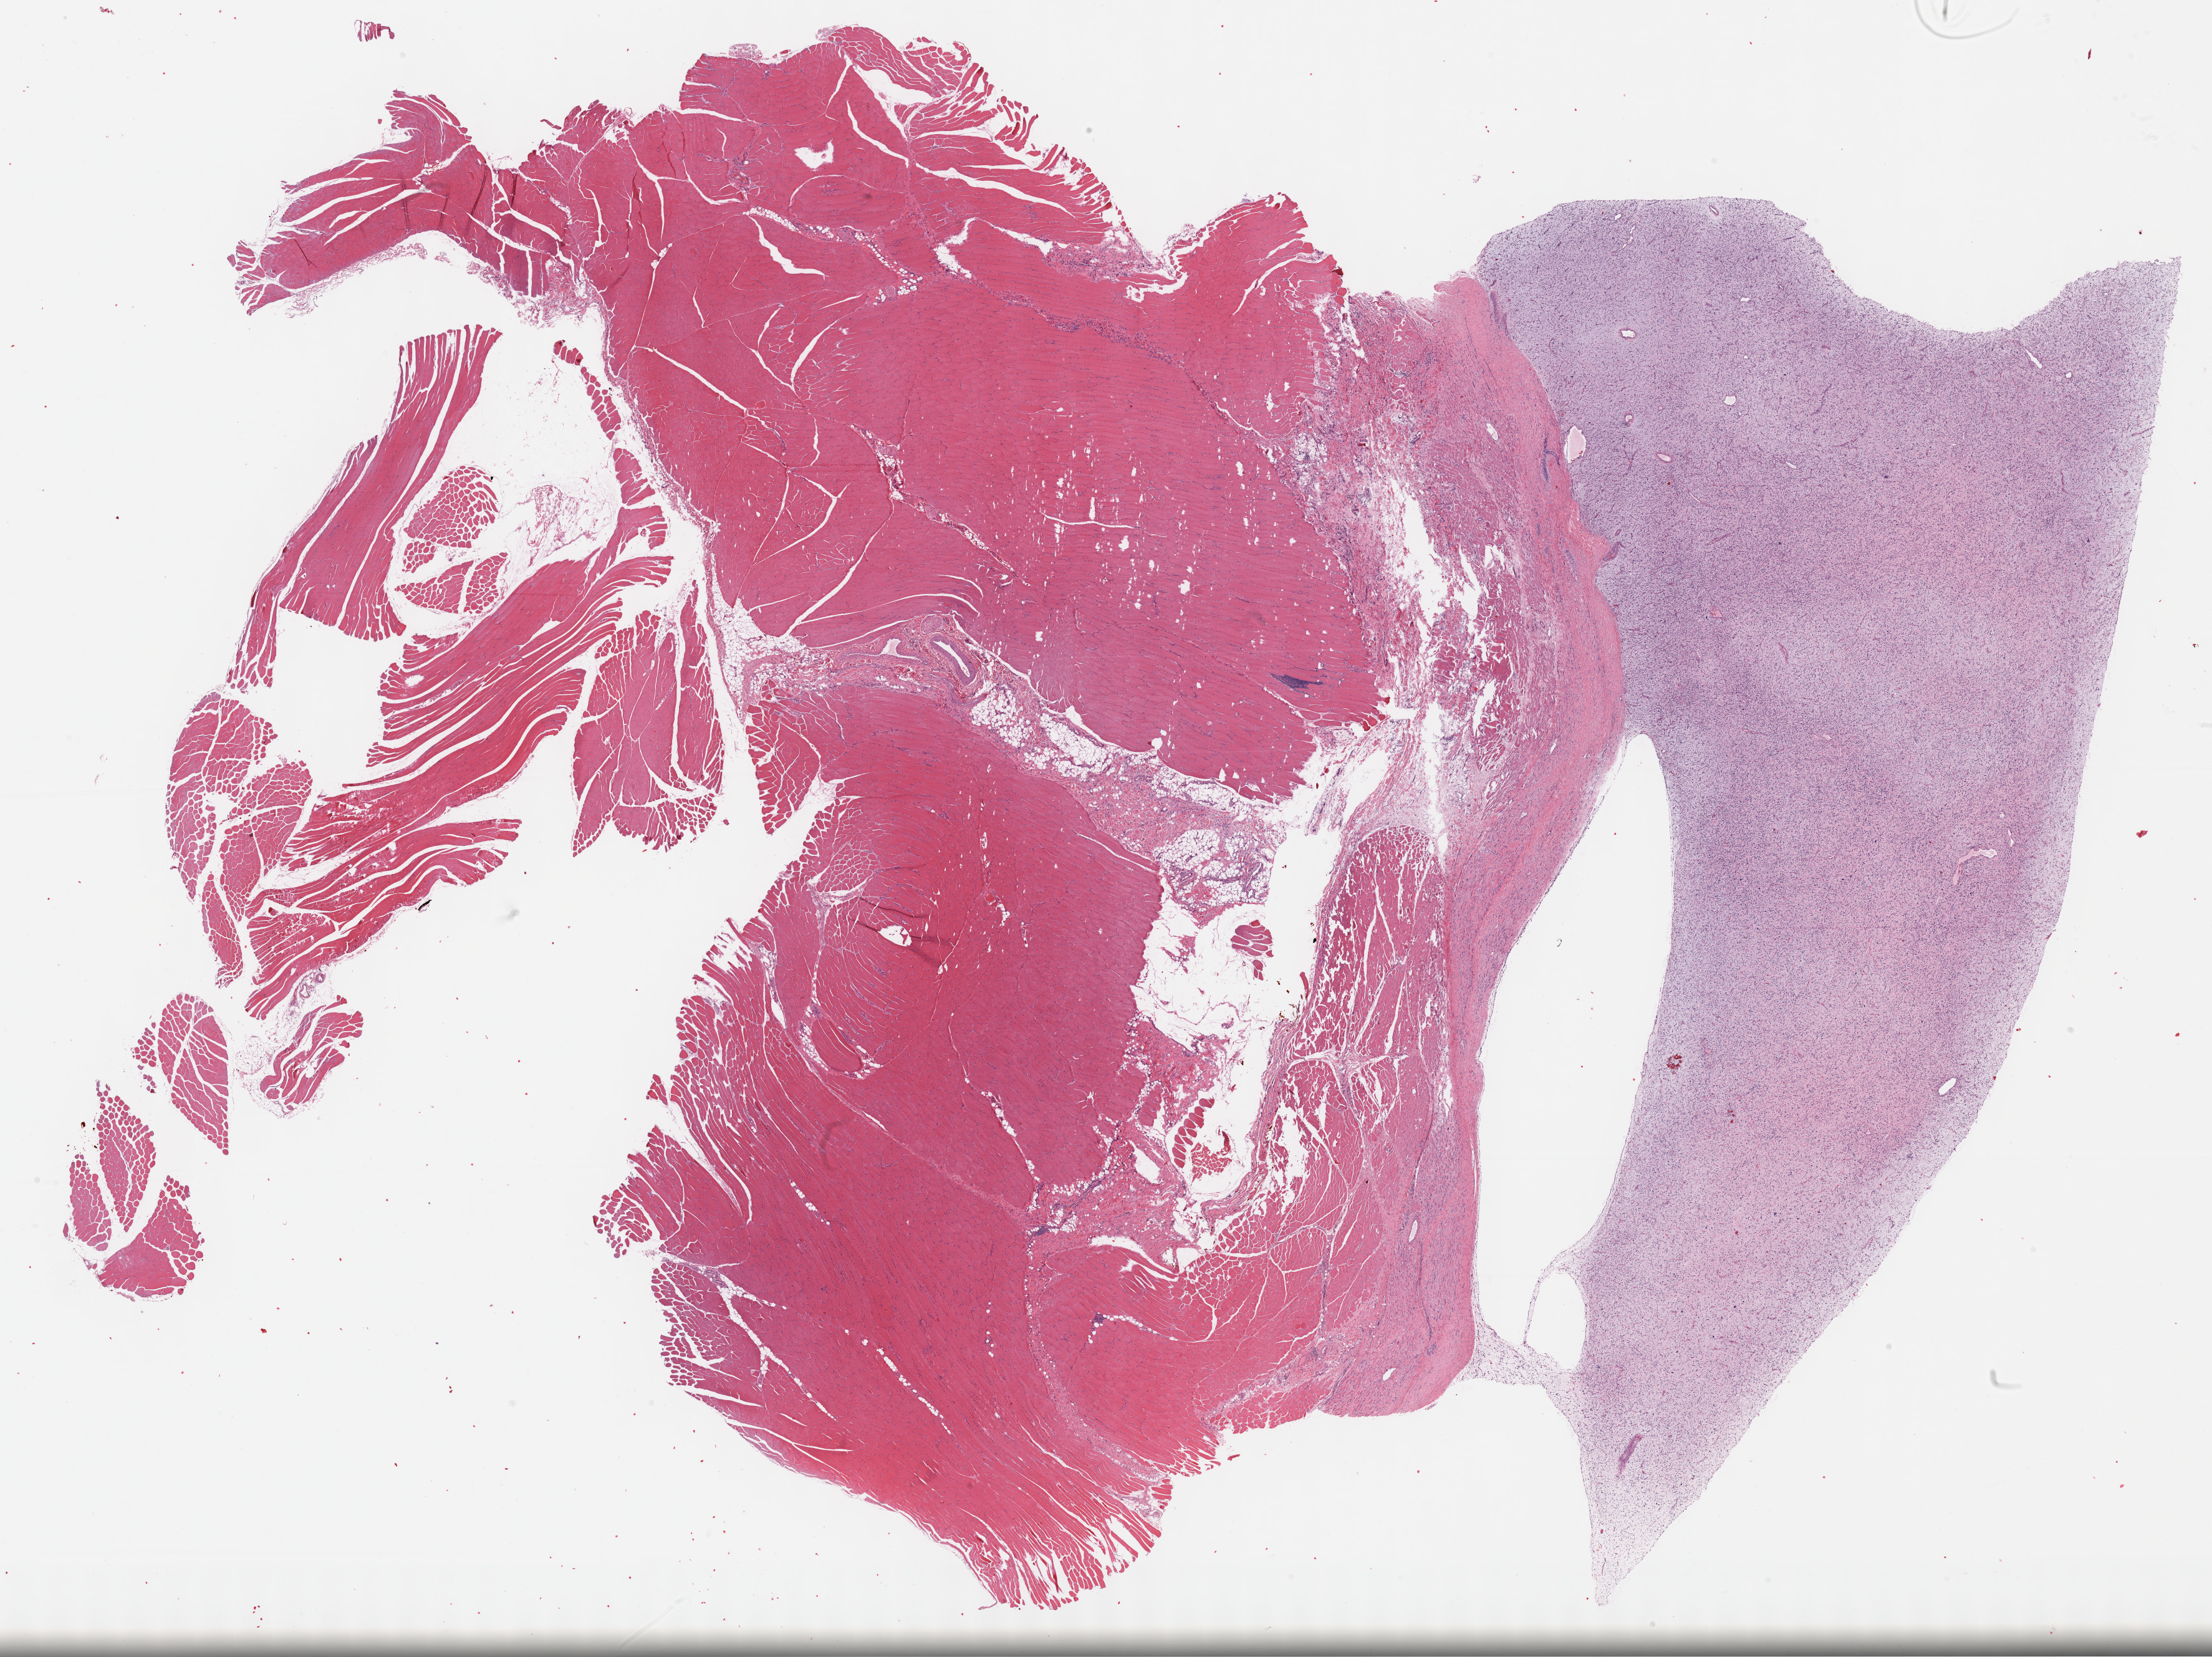
H&E-stained whole-slide image — whole scanned area (about 28.7 x 21.5 mm) shown as a low-resolution overview, formalin-fixed paraffin-embedded (FFPE) diagnostic section, sample: primary tumour, connective, subcutaneous and other soft tissues. Male patient; age at initial diagnosis 35 years.
Diagnosis: Fibromyxosarcoma (connective, subcutaneous and other soft tissues of lower limb and hip).